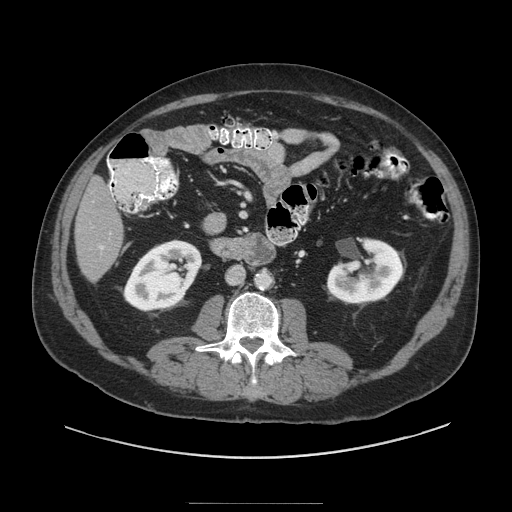
Contrast-enhanced abdominal CT (liver protocol), one axial slice; position 24 of 91 along the scan axis; 140 kVp; soft-tissue window (W 400 / L 40 HU); 2.5 mm slice thickness; 512 × 512 image matrix. Case-level facts recorded for this patient, not image findings: diagnosis: hepatocellular carcinoma (patient treated with transarterial chemoembolisation; whether this scan precedes or follows treatment is not stated here); TNM stage (as recorded): Stage-I; Child-Pugh class: A; tumour differentiation: well differentiated.
Outlined on this slice (semi-automatically segmented with operator editing):
- liver parenchyma outside the tumour (the mass and vessels are separate outlines, so this box may not span the whole liver): box from (x=74, y=176) to (x=122, y=281) px
- liver vessels: (x=99, y=245)–(x=104, y=250)